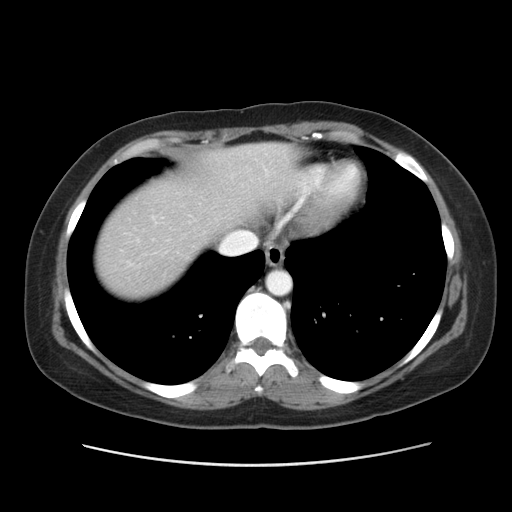
Contrast-enhanced abdominal CT, one axial slice. Reconstruction kernel STANDARD. 120 kVp. Intravenous contrast given. Soft-tissue window (W 400 / L 40 HU). 5 mm slice thickness. 512 × 512 image matrix. Female patient, age 48 years. Case-level facts recorded for this patient, not image findings: diagnosis: colorectal cancer liver metastases, imaged before liver resection; multiple liver metastases: yes.
Annotated regions visible in this slice (manually delineated by an expert):
- hepatic veins: bounding box (x1, y1, x2, y2) in pixels: (220, 231, 257, 252)
- liver: (97, 145, 299, 293)
- planned liver remnant (the part of the liver to remain after resection): (172, 145, 300, 228)